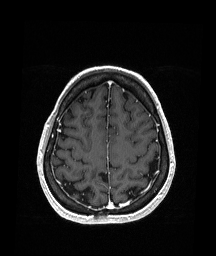
Brain MRI from a brain-tumour surgery series, one axial slice; slice 56 of 151 in the series (ordered by position); T1-weighted post-contrast; 1.05 mm slice thickness; 216 × 256 image matrix, field of view 211 × 250 mm. From the clinical record (not read from this slice): histopathology: Oligodendroglioma; WHO grade: 2; IDH mutation: yes.
Structures marked on this image (expert manual segmentation):
- previous resection cavity: box from (x=94, y=170) to (x=109, y=180) px